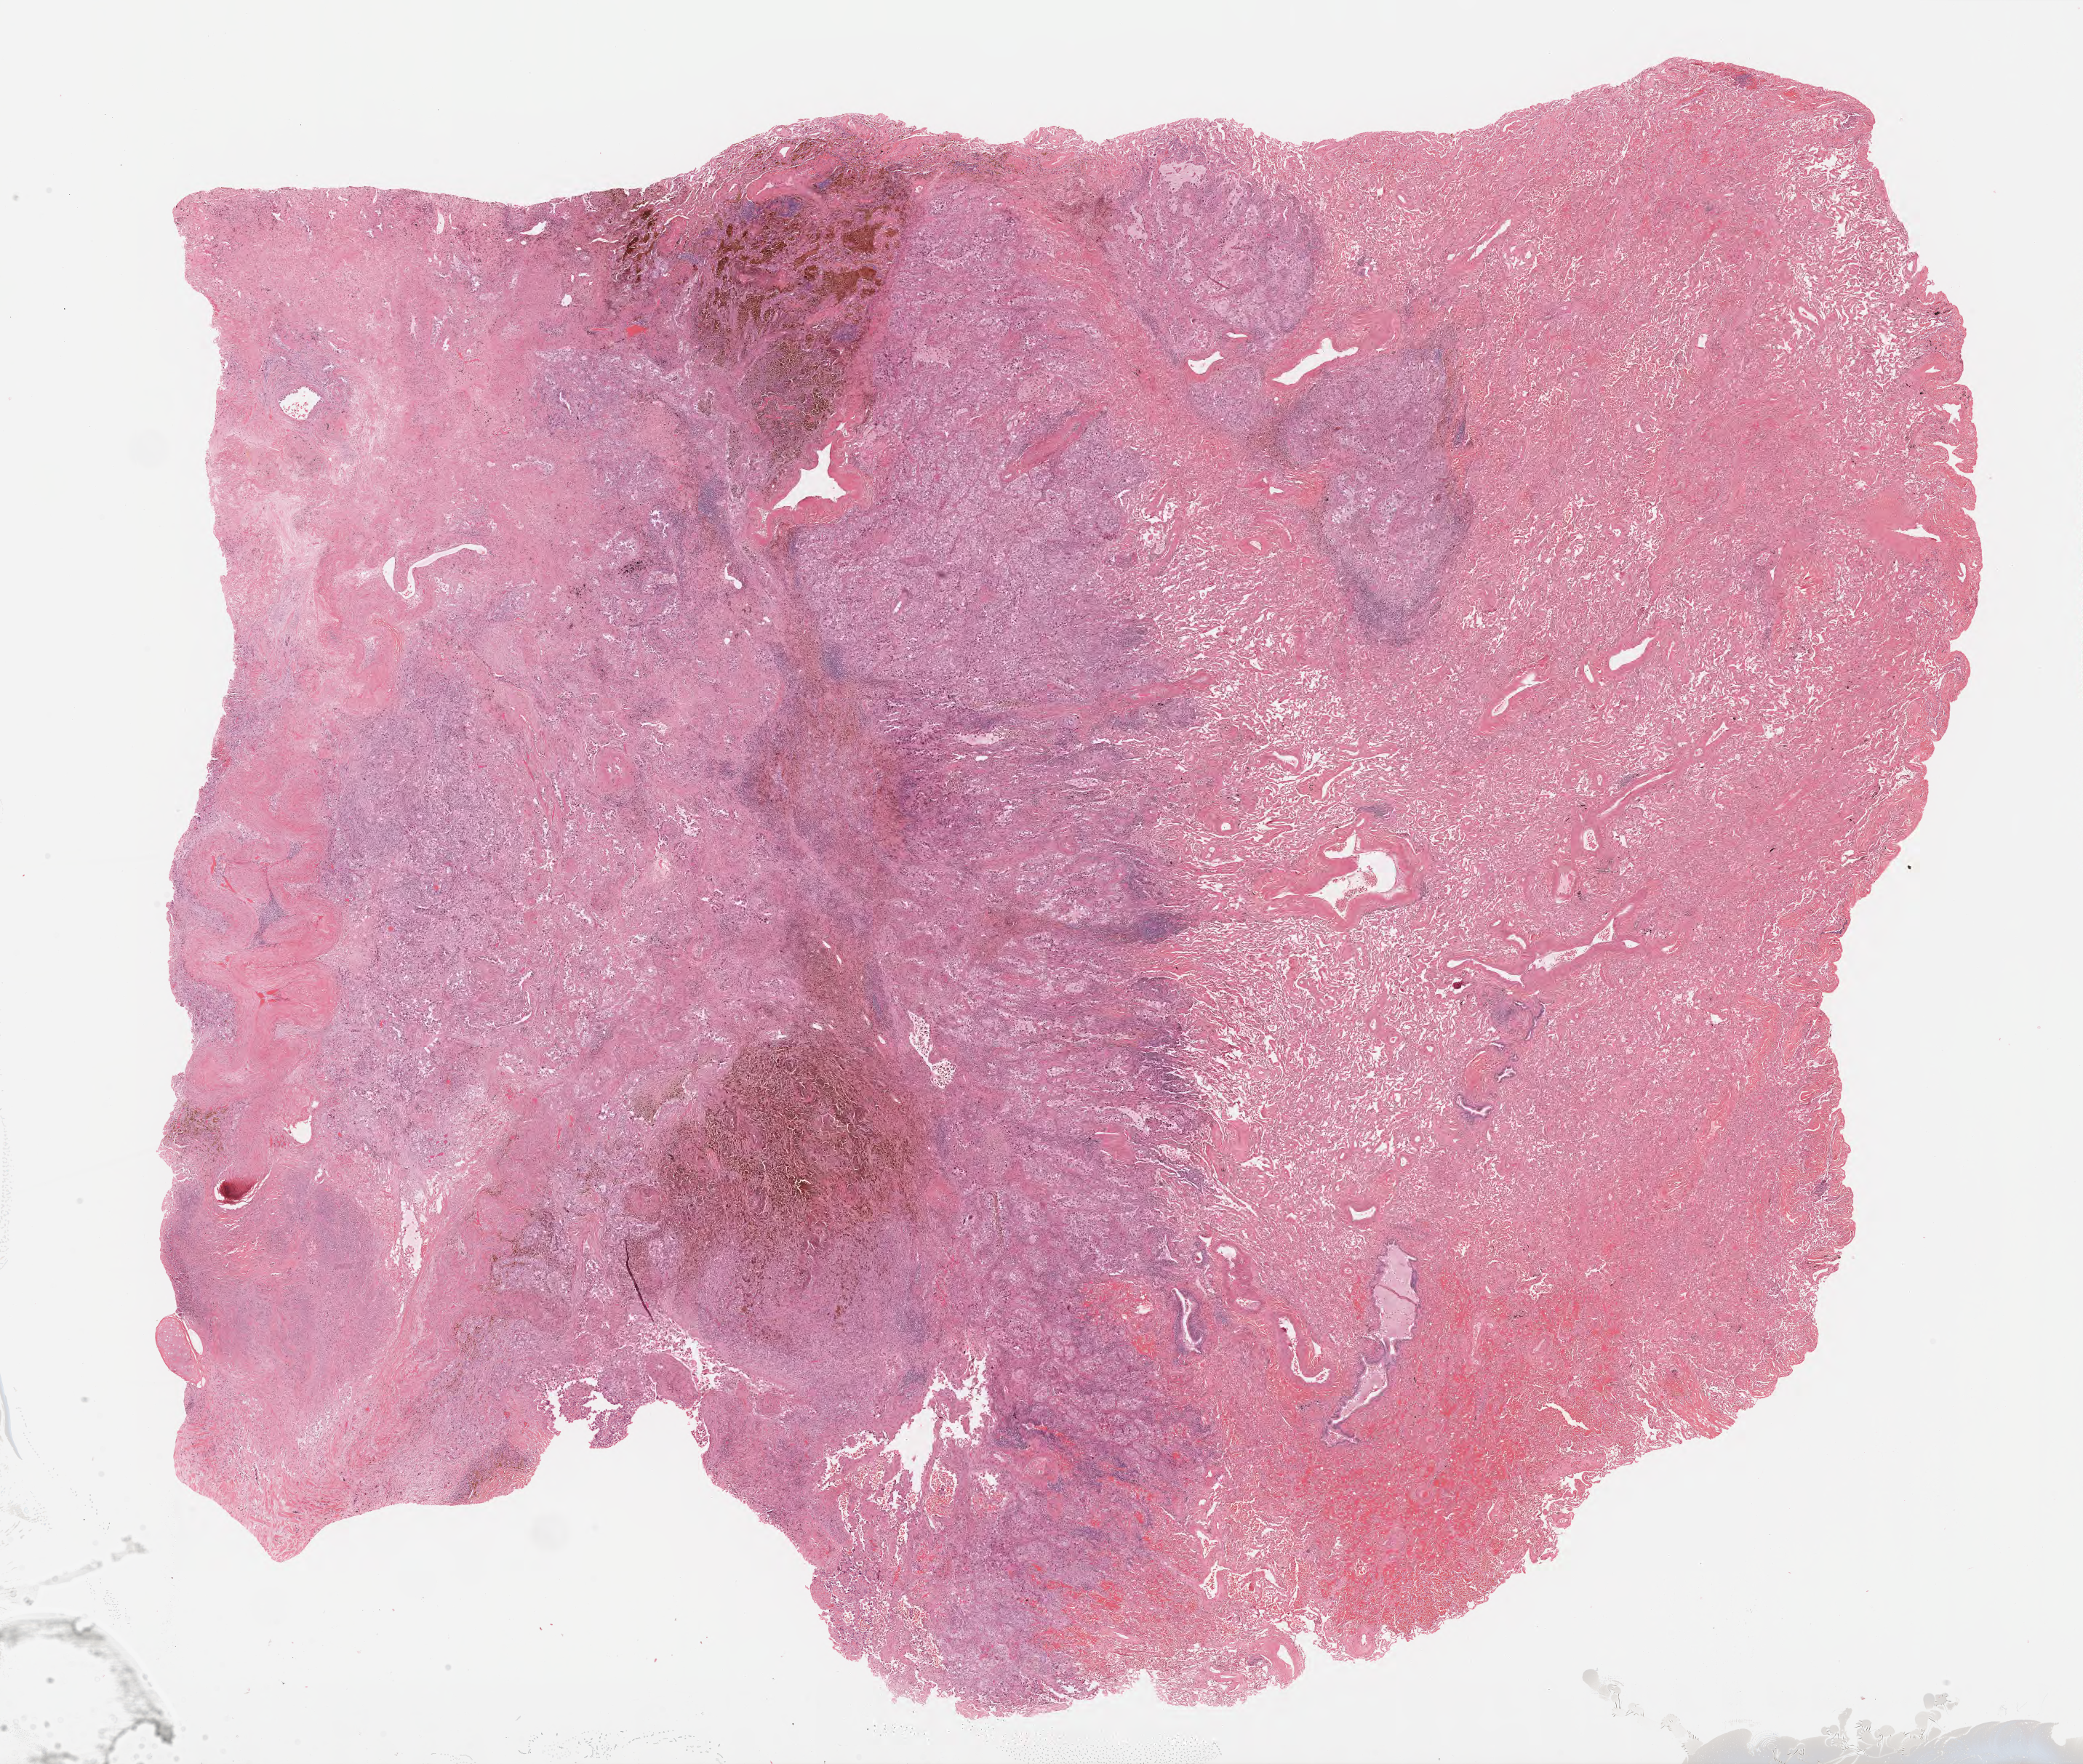
Whole-slide histology image, Hematoxylin and eosin (H&E) stained, shown as a low-resolution overview of the whole scanned area (about 23.1 x 19.6 mm, acquisition: 40x scan). Formalin-fixed paraffin-embedded (FFPE) diagnostic section. Lung, primary tumour sample. Female, age 56 years at initial diagnosis.
Histologic diagnosis: Adenocarcinoma, NOS (lower lobe, lung).